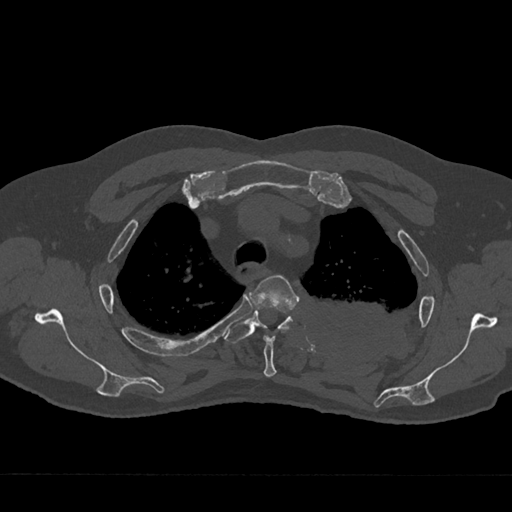
CT including the spine, one axial slice; position 544 of 797 along the scan axis; reconstruction kernel Br40s/3; bone window (W 1800 / L 400 HU); 0.5 mm slice thickness; 512 × 512 image matrix. Patient: male, 75 years. Case-level facts recorded for this patient, not image findings: primary cancer: renal; vertebrae with lytic lesions (as recorded): T4.
Outlined on this slice (semi-automatic segmentation, software-assisted and operator-edited):
- T3 vertebra: box from (x=249, y=275) to (x=298, y=377) px
- T4 vertebra: (x=224, y=309)–(x=293, y=344)